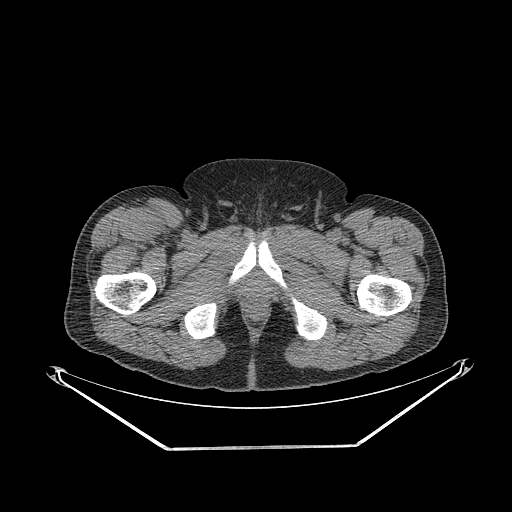
CT of an extremity soft-tissue mass (from a PET/CT study), one axial slice; position 308 of 311 along the scan axis; reconstruction kernel STANDARD; 140 kVp; soft-tissue window (W 400 / L 40 HU); 3.75 mm slice thickness; 512 × 512 image matrix, field of view 500 × 500 mm. Male patient. Case-level facts recorded for this patient, not image findings: histological type: pleiomorphic leiomyosarcoma; grade: intermediate; site of the primary tumour: right thigh.
Annotated regions visible in this slice (expert contour drawn on MRI and transferred to this co-registered scan by the dataset authors):
- gross tumour volume including surrounding oedema: bounding box (x1, y1, x2, y2) in pixels: (142, 208, 168, 238)